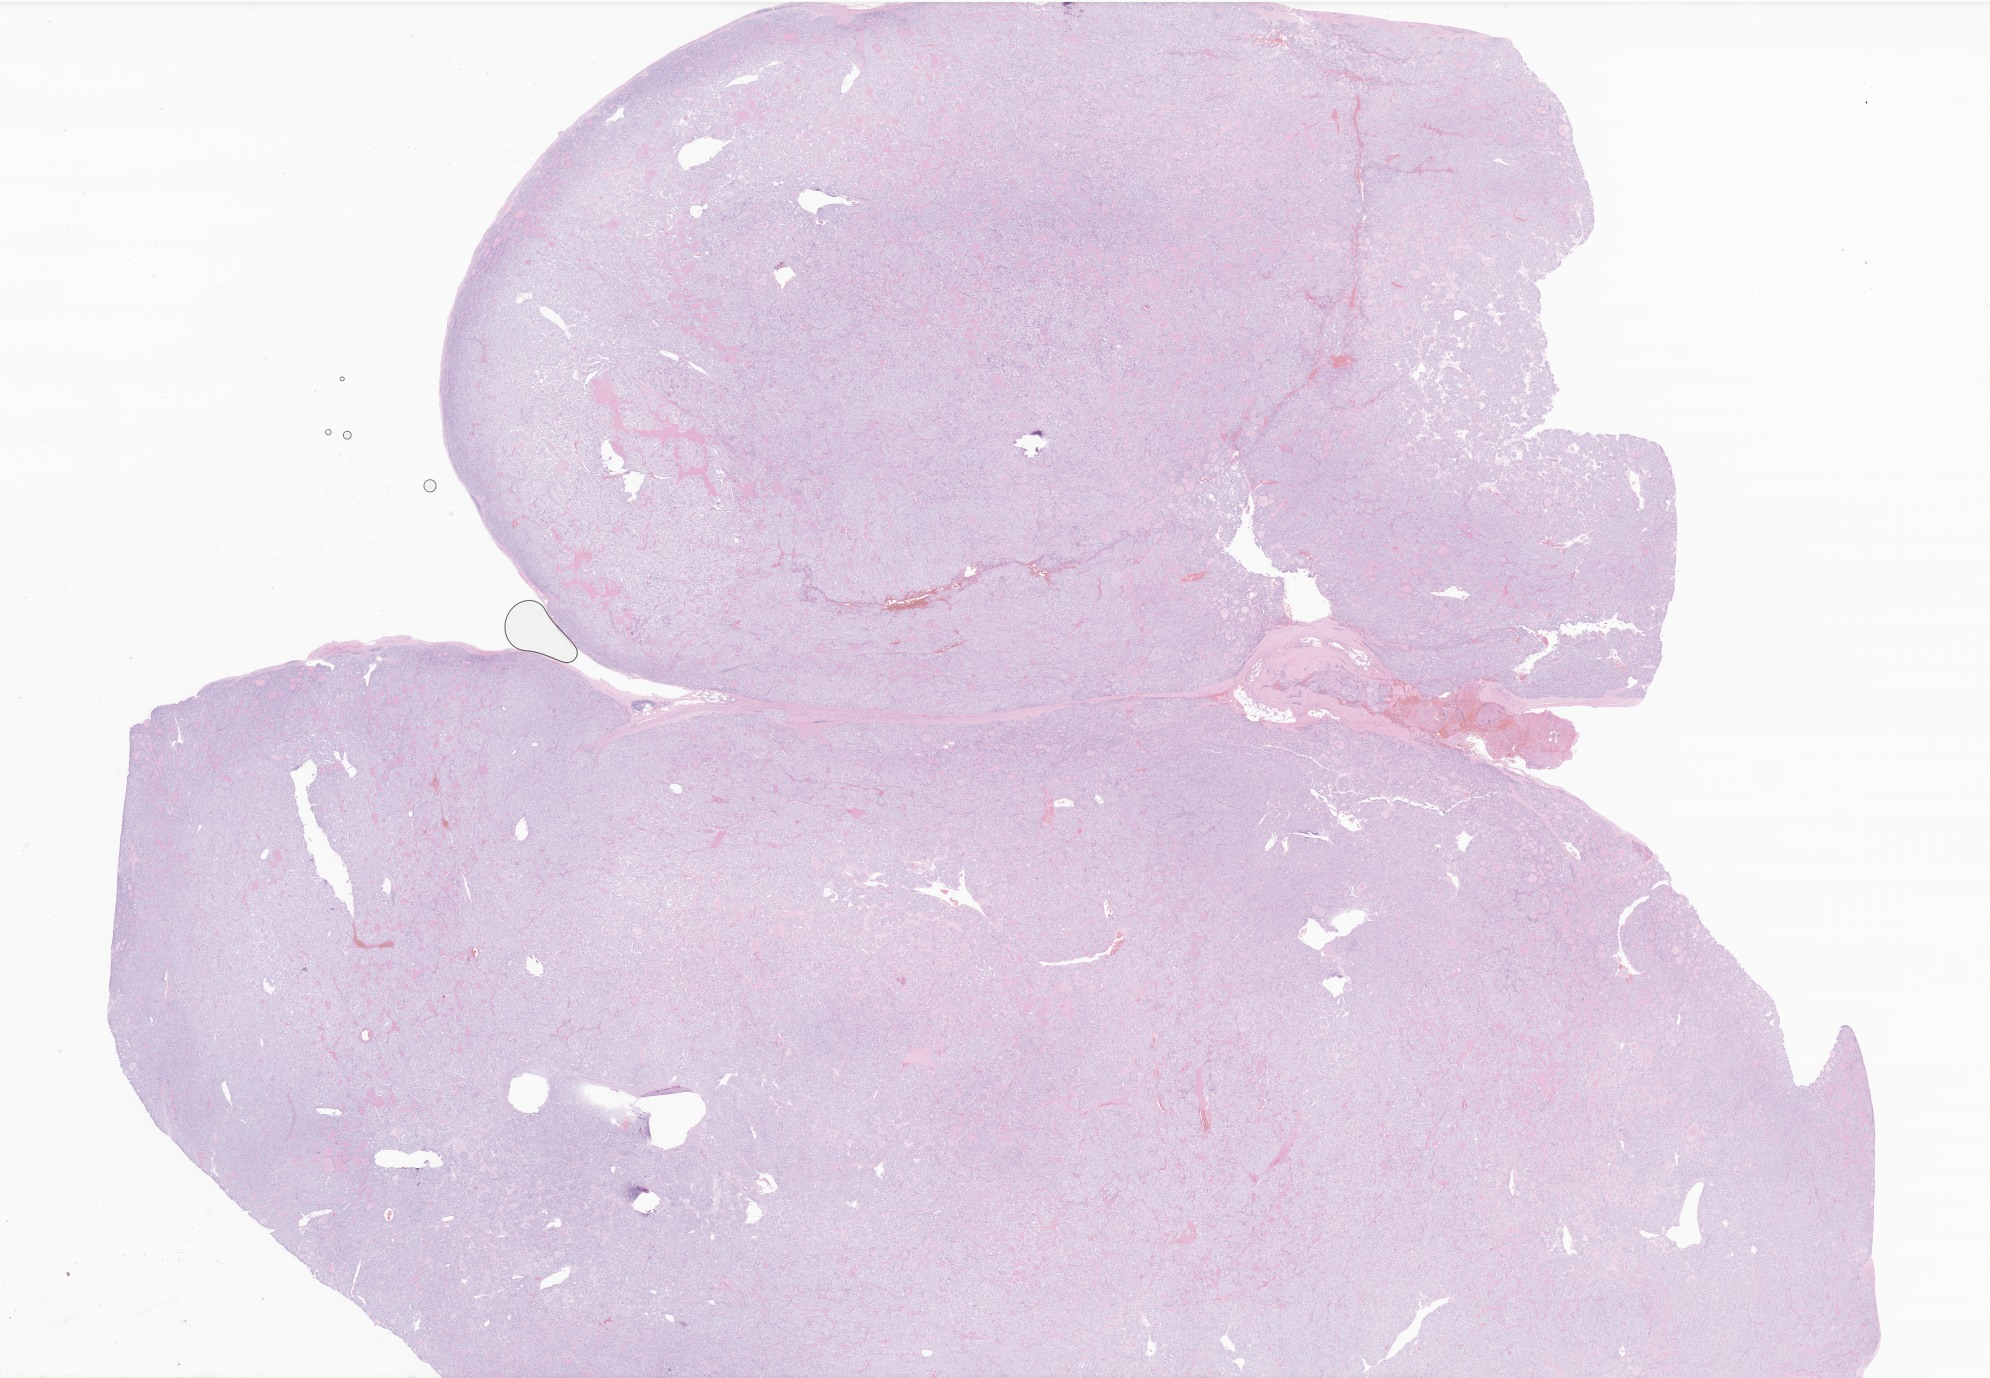
Whole-slide image, haematoxylin and eosin stain of tumor tissue from the thyroid — a low-resolution overview of the entire scanned area, about 33.6 x 23.2 mm. Formalin-fixed paraffin-embedded section. Male patient, age 235 months (19 years 7 months).
Recorded diagnosis: Papillary carcinoma, NOS.